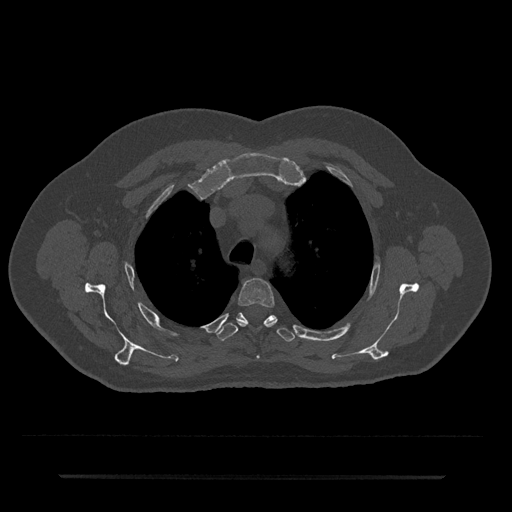
CT including the spine, one axial slice. Position 551 of 797 along the scan axis. Reconstruction kernel Br40s/3. Bone window (W 1800 / L 400 HU). 0.5 mm slice thickness. 512 × 512 image matrix, field of view 437 × 437 mm. Male patient, age 69 years. From the clinical record (not read from this slice): primary cancer: prostate.
Structures marked on this image (semi-automatically segmented with operator editing):
- T3 vertebra: box from (x=236, y=278) to (x=277, y=358) px
- T4 vertebra: (x=216, y=313)–(x=295, y=342)